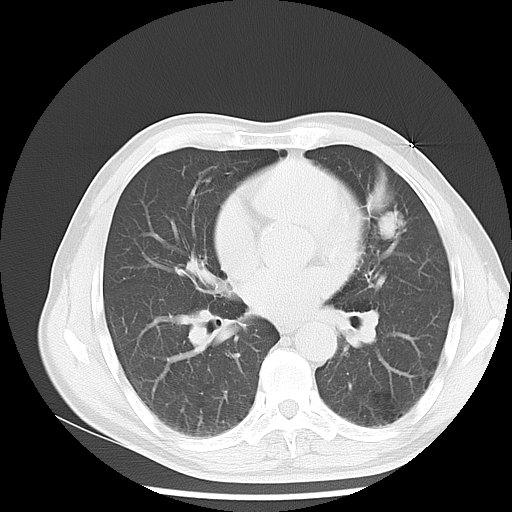
Chest CT, one axial slice; slice 5 of 13 in the series (ordered by position); 120 kVp; lung window (W 1500 / L -600 HU); 5 mm slice thickness; 512 × 512 image matrix, field of view 350 × 350 mm. Male patient, age 54 years. Case-level facts recorded for this patient, not image findings: clinical TNM (as recorded): T1c N0 M0.
Outlined on this slice (bounding box drawn by a radiologist):
- lung tumour (recorded histology: adenocarcinoma): bounding box (x1, y1, x2, y2) in pixels: (363, 192, 407, 250)